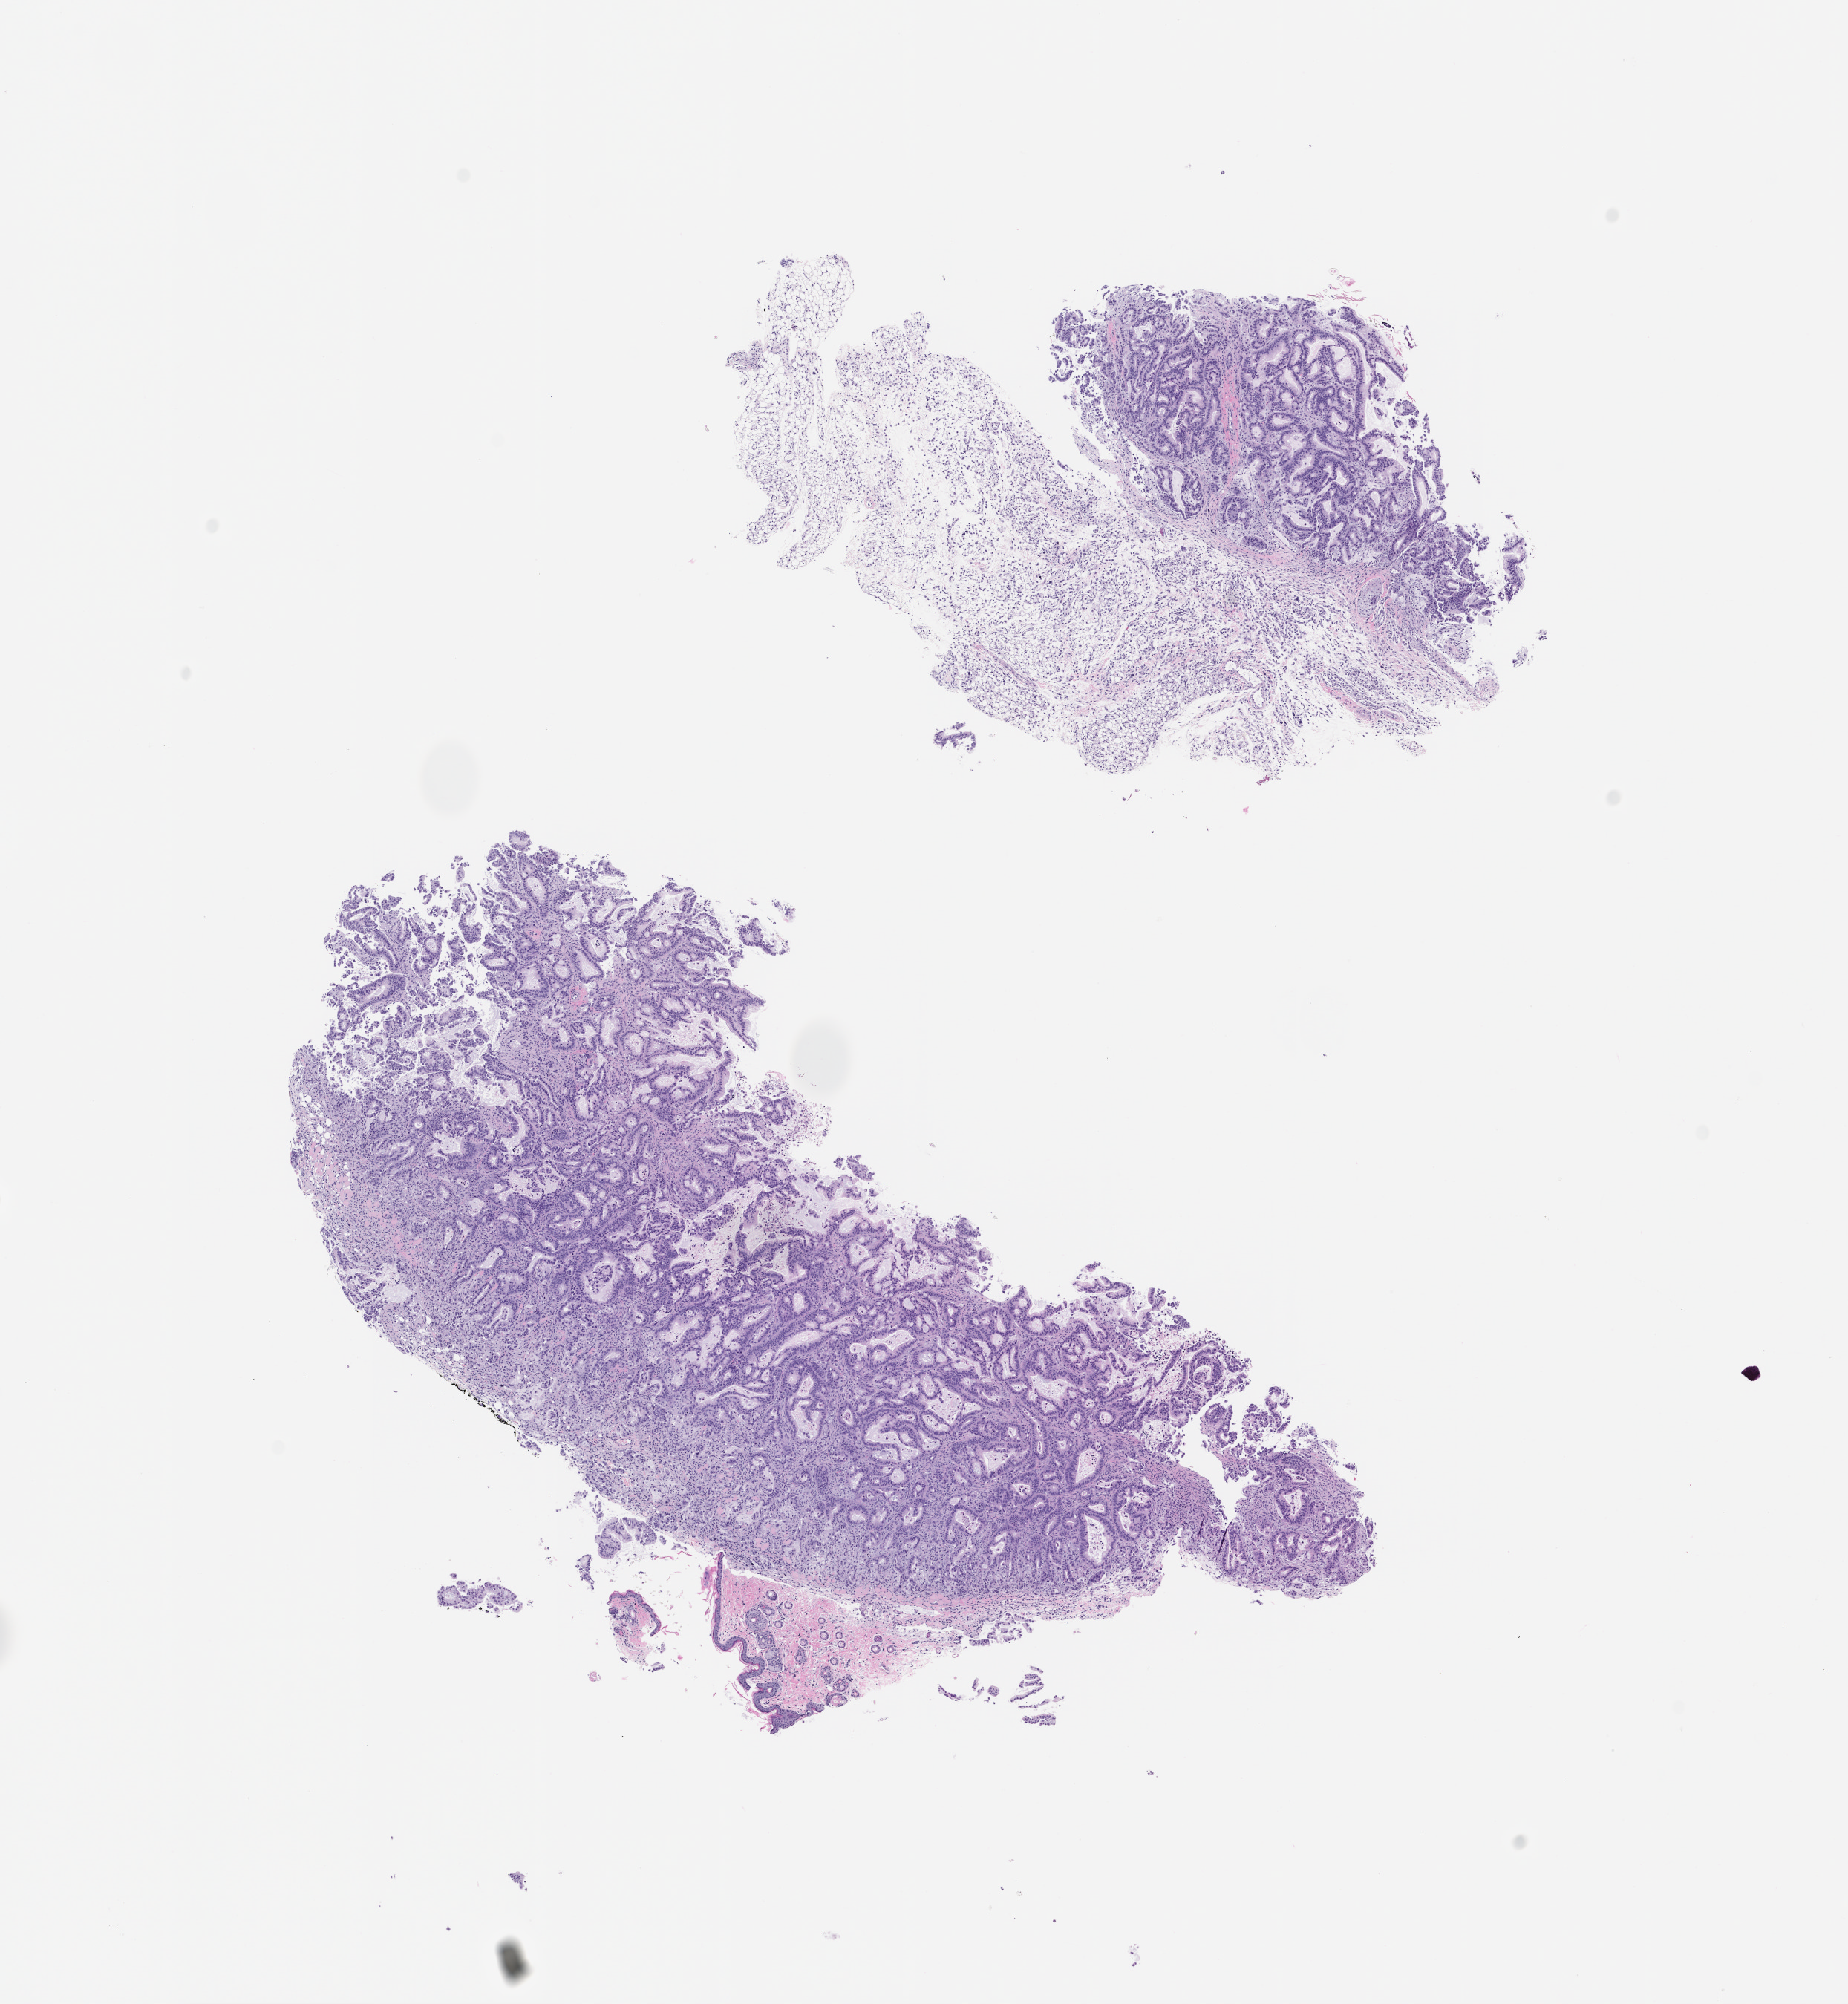
Hematoxylin and eosin (H&E) whole-slide image of a patient-derived xenograft (PDX) tumor grown in a mouse, passage 1 — a low-resolution overview of the entire scanned area, about 10.0 x 10.8 mm. Formalin-fixed, paraffin-embedded (FFPE) tissue. Tumor site category: pancreas.
Originating patient diagnosis: Pancreatic Adenocarcinoma.